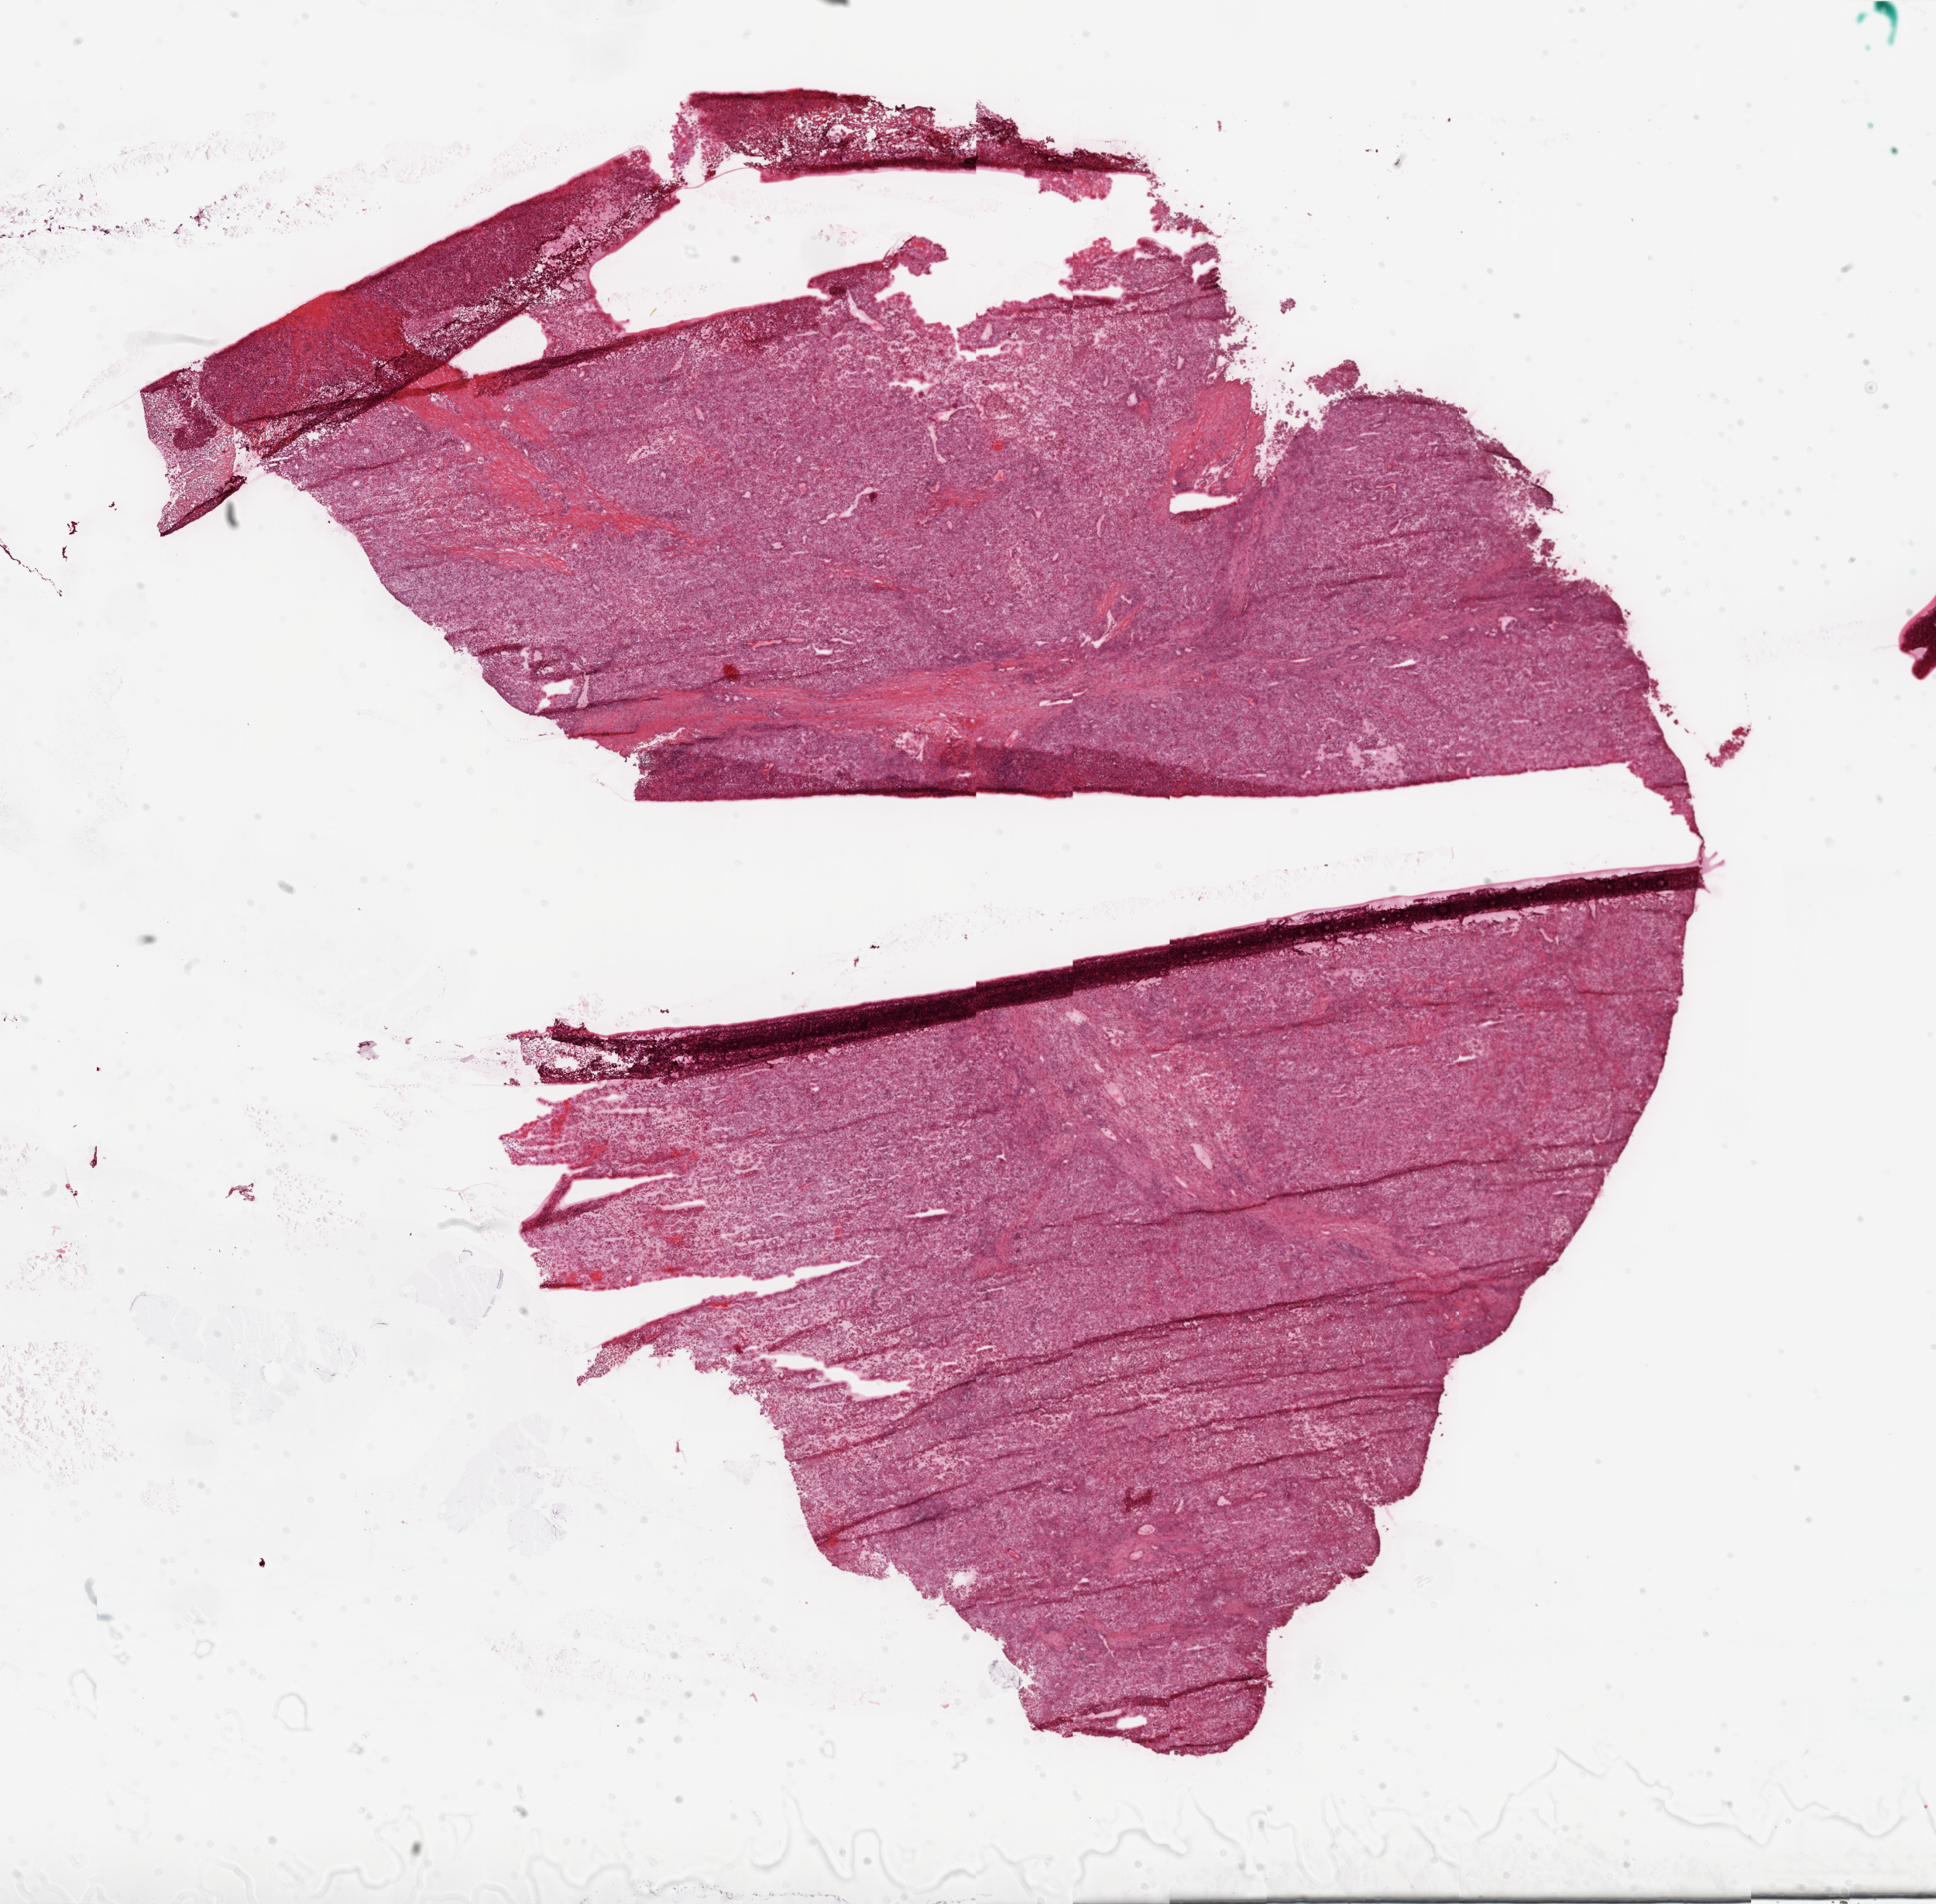
Digitized H&E-stained tissue section (whole slide), low-resolution overview of the scanned area, about 20.1 x 19.7 mm (slide scanned at 20x), frozen section, primary tumour sample from the kidney. Patient: female, age at initial diagnosis 67 years. Histologic grade: G4 (undifferentiated). Composition of this section per pathologist review: tumour cells 90%, tumour nuclei 85%, normal cells 0%, stromal cells 10%, necrosis 0%.
• AJCC pathologic stage: III
• pathologic diagnosis: Clear cell adenocarcinoma, NOS